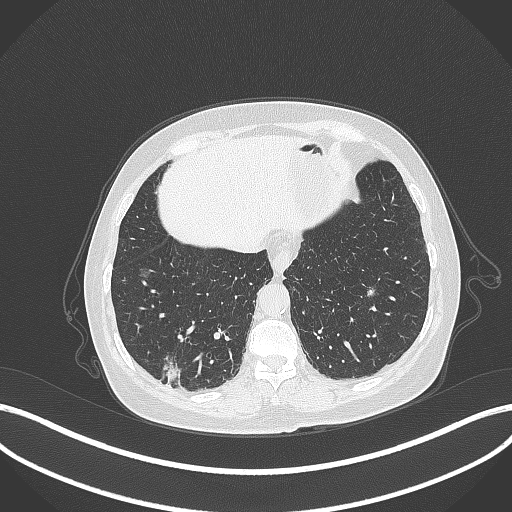
Chest CT, one axial slice; position 67 of 333 along the scan axis; lung window (W 1500 / L -600 HU); 512 × 512 image matrix, field of view 400 × 400 mm. Patient: female, 69 years. Case-level facts recorded for this patient, not image findings: clinical TNM (as recorded): T1b N0 M0; histopathological grade: G2-3.
Annotated regions visible in this slice (bounding box drawn by a radiologist):
- lung tumour (recorded histology: adenocarcinoma): bounding box (x1, y1, x2, y2) in pixels: (158, 357, 183, 382)